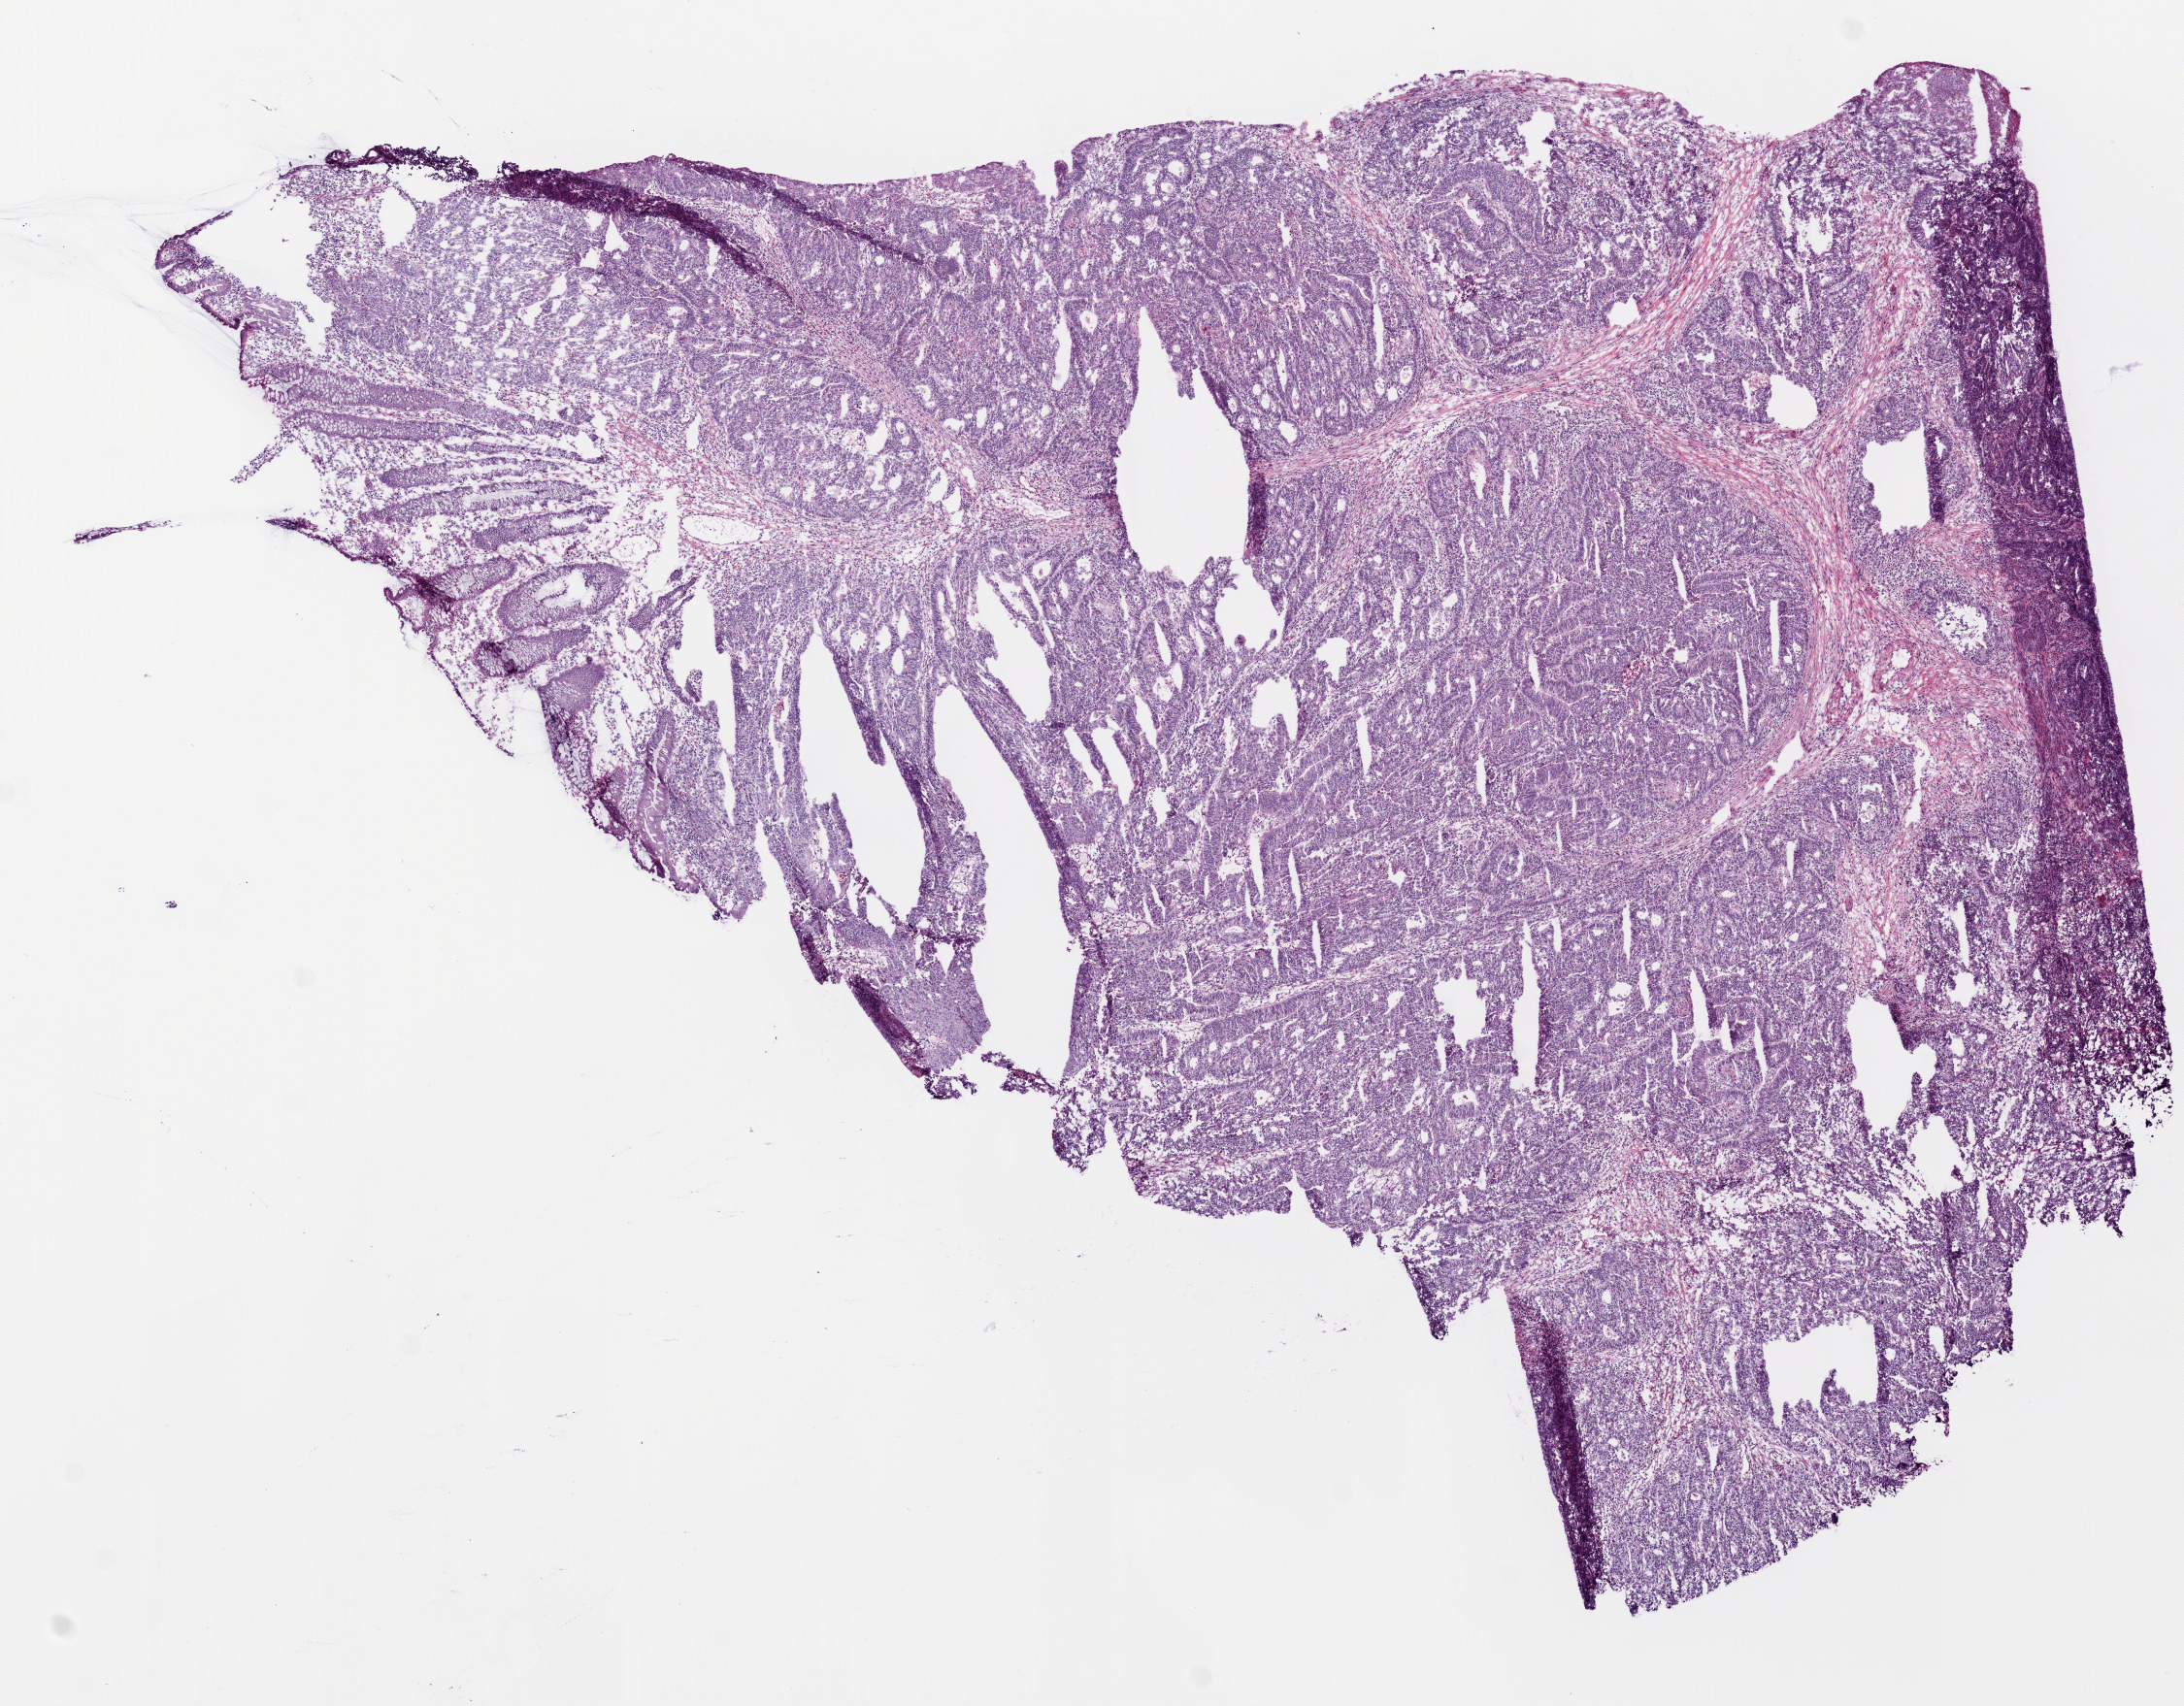
Hematoxylin and eosin (H&E) stained whole-slide image, a low-resolution overview of the entire scanned area, about 9.0 x 7.1 mm (from a 20x scan). Frozen section from the bottom of the tissue portion. Rectum, primary tumour sample. Patient: female, age at initial diagnosis 79 years.
Diagnosis: Adenocarcinoma, NOS.